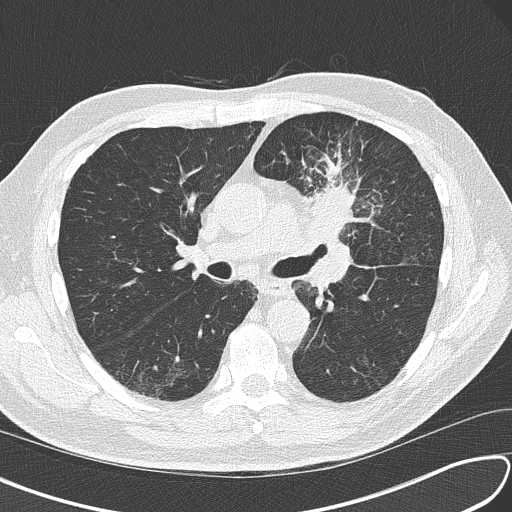
Chest CT (low-dose screening protocol), one axial image, third annual screen, lung window (W 1500 / L -600 HU), 2 mm slice thickness, lung (sharp) reconstruction kernel (B50f), slice 65 of 156 in the series, 512 × 512 image matrix. Male participant, aged 67 years at enrolment. Current smoker at enrolment.
- Lesion marked by an expert reader, bounding box <294,161,394,251> (left, top, right, bottom; pixels).
- Reader record for this screening exam (exam-level; its link to the box is not recorded): non-calcified nodule or mass ≥4 mm, left upper lobe, 30 × 23 mm, soft tissue attenuation, pre-existing on the prior screen: no.
- Participant outcome: lung cancer diagnosed 41 days after this screen — small cell carcinoma, NOS, left upper lobe, stage IV (AJCC 6th edition), 30 mm at pathology.